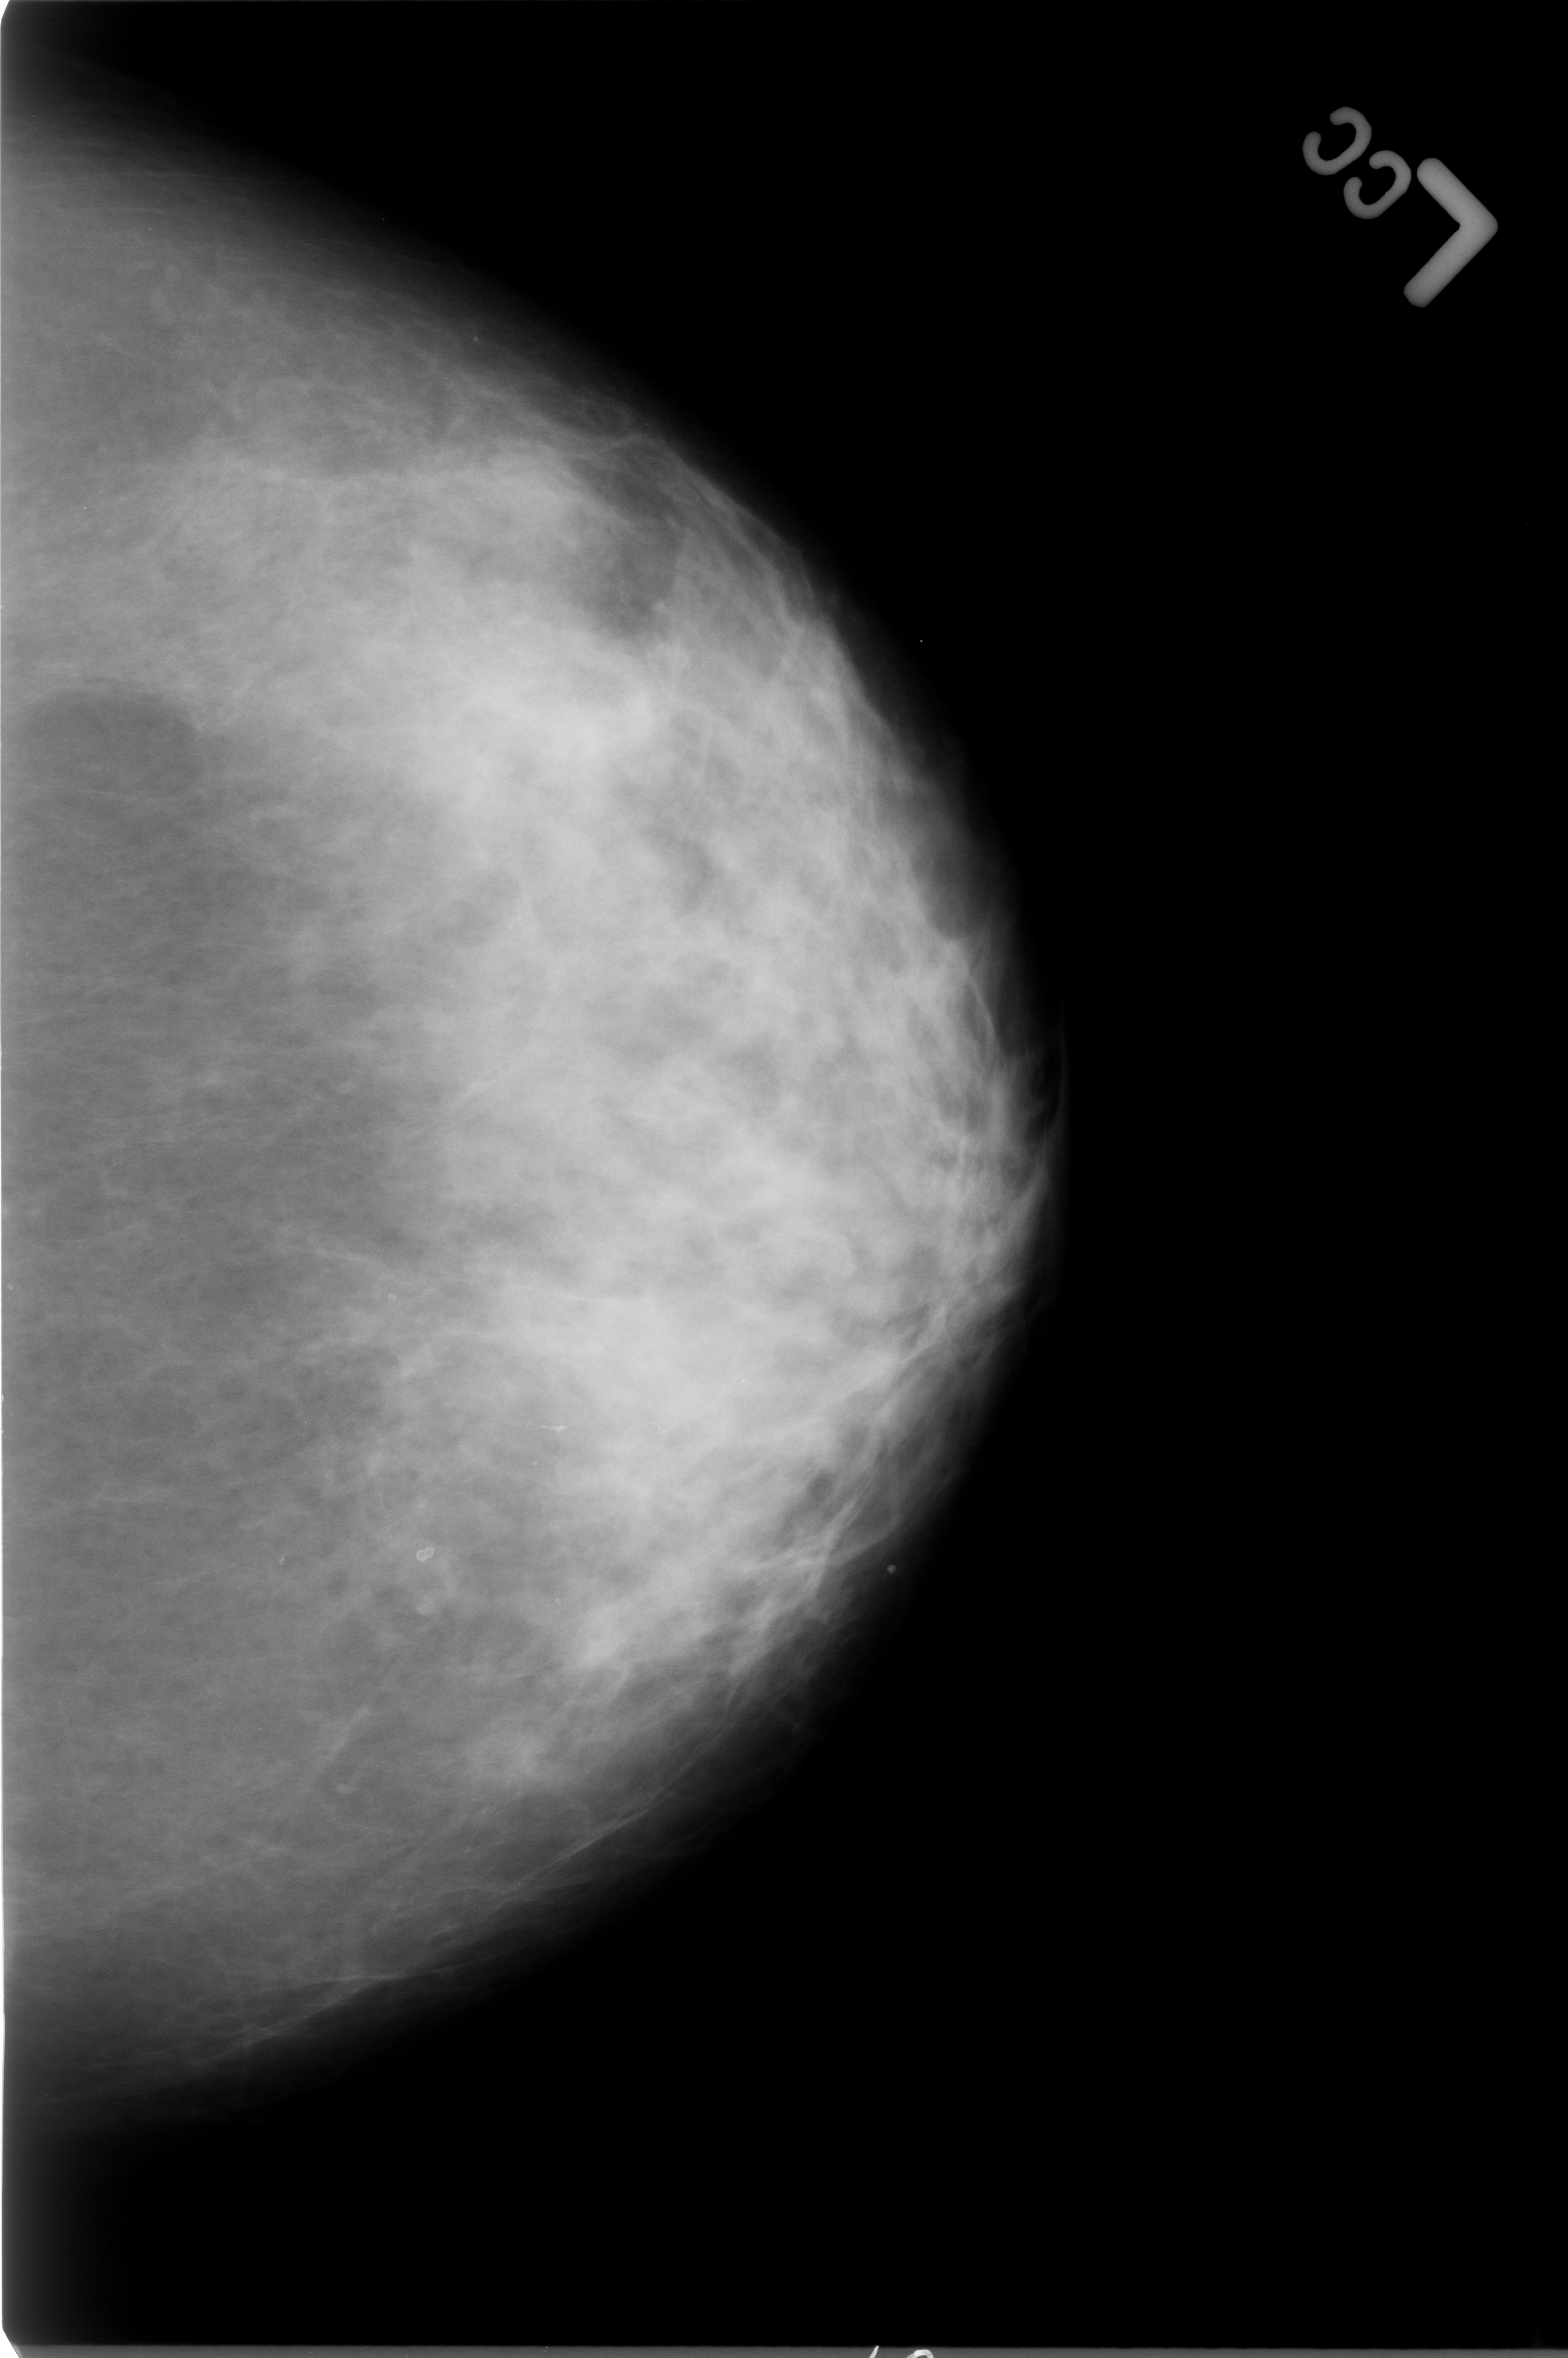
Mammogram (digitized film), left breast, craniocaudal (CC) view, breast composition: heterogeneously dense (BI-RADS density category 3 of 4).
Radiologist-marked abnormalities on this image: Finding 1 of 2: calcifications, morphology round and regular / lucent centered; BI-RADS assessment category 2; benign without callback (not worked up further). Finding 2 of 2: calcifications, morphology round and regular / lucent centered; BI-RADS assessment category 2; benign without callback (not worked up further).